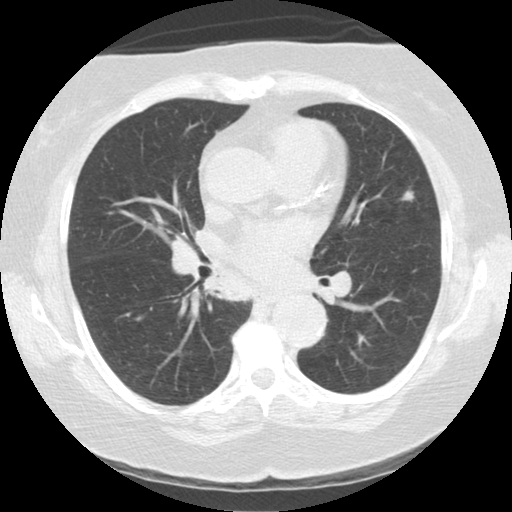
Low-dose screening chest CT, one axial slice; slice 72 of 122 in the series (ordered by position); reconstruction kernel STANDARD; lung window (W 1500 / L -600 HU); 2.5 mm slice thickness; 512 × 512 image matrix, field of view 329 × 329 mm.
Structures marked on this image (outlined manually by an expert reader):
- lesion 2 (nodule, upper lobe of left lung): bounding box [x1, y1, x2, y2] px = [403, 189, 414, 202]